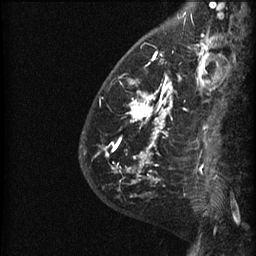
Breast MRI (dynamic contrast-enhanced), one sagittal slice. Slice 14 of 60 in the series (ordered by position). Dynamic contrast-enhanced series, image 2 of 3 at this slice position (ordered by acquisition). 1.5 T. TE 4.2 ms, TR 22.7 ms. 256 × 256 image matrix, field of view 180 × 180 mm. Patient: female, 48 years. Case-level facts recorded for this patient, not image findings: setting: breast cancer imaged before/during neoadjuvant chemotherapy; receptor status: triple-negative.
Structures marked on this image (semi-automatic segmentation, software-assisted and operator-edited):
- analysis volume of interest (the breast-tissue region the enhancement analysis was run in; not a lesion): bounding box (x1, y1, x2, y2) in pixels: (89, 27, 191, 180)
- tumour enhancement mask (voxels above the 90 % enhancement threshold inside the analysis volume of interest): (108, 53, 174, 180)